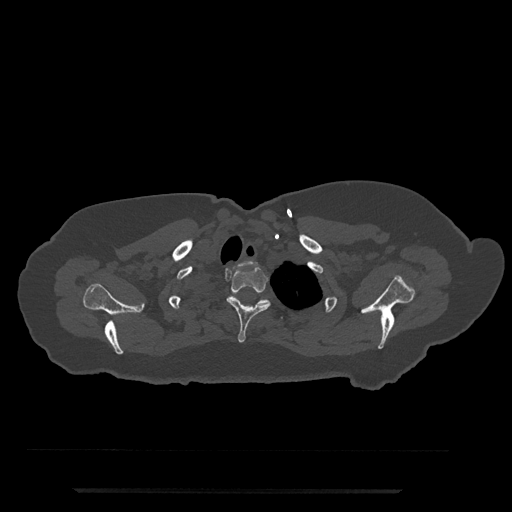
CT including the spine, one axial slice. Reconstruction kernel Br40s/3. 120 kVp. Bone window (W 1800 / L 400 HU). 0.5 mm slice thickness. 512 × 512 image matrix, field of view 440 × 440 mm. Patient: female, 51 years. Case-level facts recorded for this patient, not image findings: primary cancer: neuro; vertebrae with lytic lesions (as recorded): T8.
Annotated regions visible in this slice (semi-automatic segmentation, software-assisted and operator-edited):
- T1 vertebra: bounding box (x1, y1, x2, y2) in pixels: (240, 261, 251, 266)
- T2 vertebra: (226, 266, 271, 343)
- T3 vertebra: (233, 292, 283, 319)